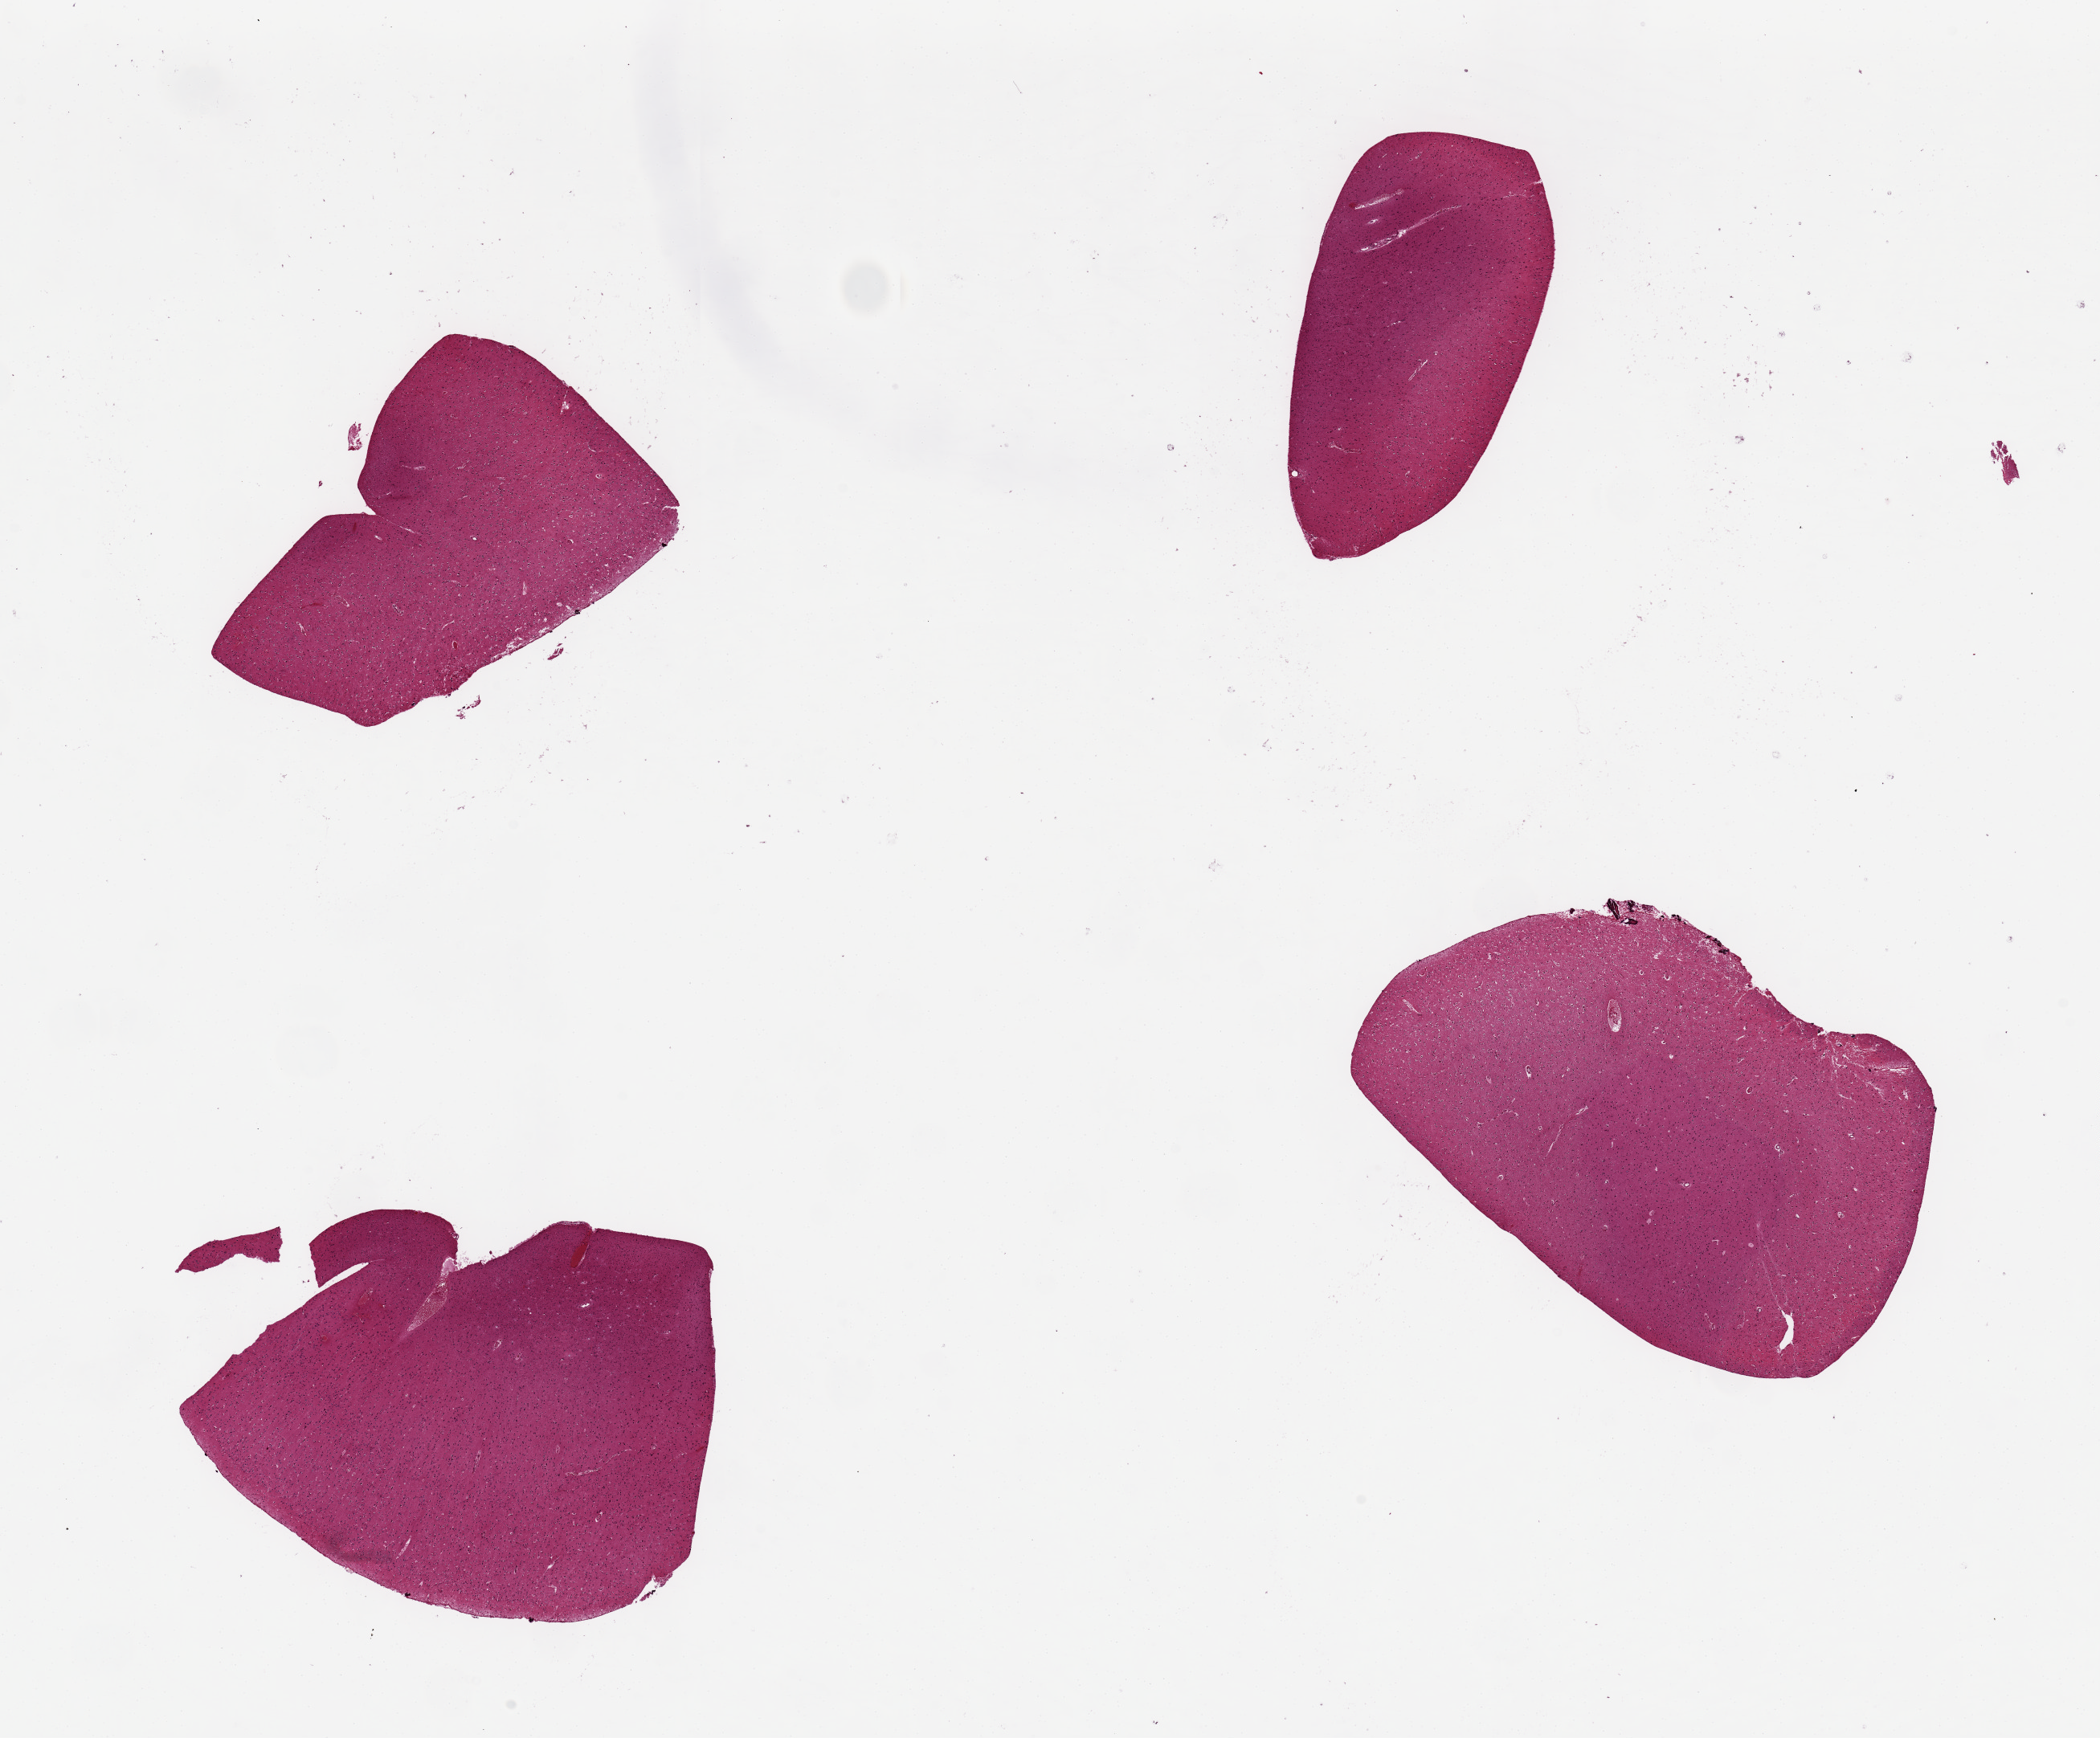
Digitized H&E-stained section, a low-resolution overview of the entire scanned area, about 20.7 x 17.1 mm (slide scanned at 20x); PAXgene-fixed paraffin-embedded (PFPE) section; section of cerebral cortex (target tissue); donor tissue sample.
Review note (as recorded): 4 pieces, ~5x3mm.